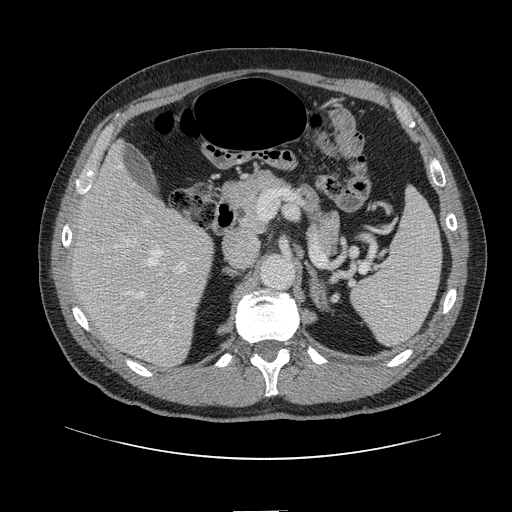
Contrast-enhanced abdominal CT, one axial slice. Slice 73 of 161 in the series (ordered by position). 120 kVp. Intravenous contrast given. Soft-tissue window (W 400 / L 40 HU). 512 × 512 image matrix, field of view 412 × 412 mm. Male patient, age 66 years. Case-level facts recorded for this patient, not image findings: diagnosis: colorectal cancer liver metastases, imaged before liver resection; multiple liver metastases: no; largest metastasis: 3.5 cm; chemotherapy before resection: yes.
Annotated regions visible in this slice (expert manual segmentation):
- hepatic veins: bounding box (x1, y1, x2, y2) in pixels: (116, 163, 172, 329)
- liver: (75, 148, 213, 366)
- planned liver remnant (the part of the liver to remain after resection): (75, 147, 192, 292)
- portal vein (with intrahepatic branches): (124, 218, 188, 304)